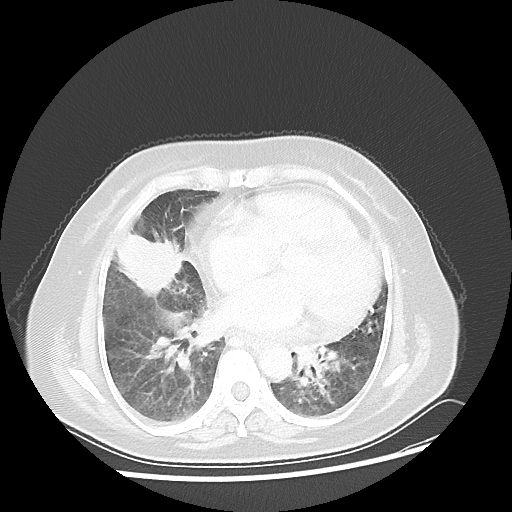
Chest CT, one axial slice; slice 19 of 45 in the series (ordered by position); lung window (W 1500 / L -600 HU); 5 mm slice thickness; 512 × 512 image matrix. Female patient, age 67 years. From the clinical record (not read from this slice): clinical TNM (as recorded): T2a N3 M1a.
Structures marked on this image (rectangle marked by the reading radiologist):
- lung tumour (recorded histology: adenocarcinoma): box from (x=119, y=227) to (x=183, y=299) px